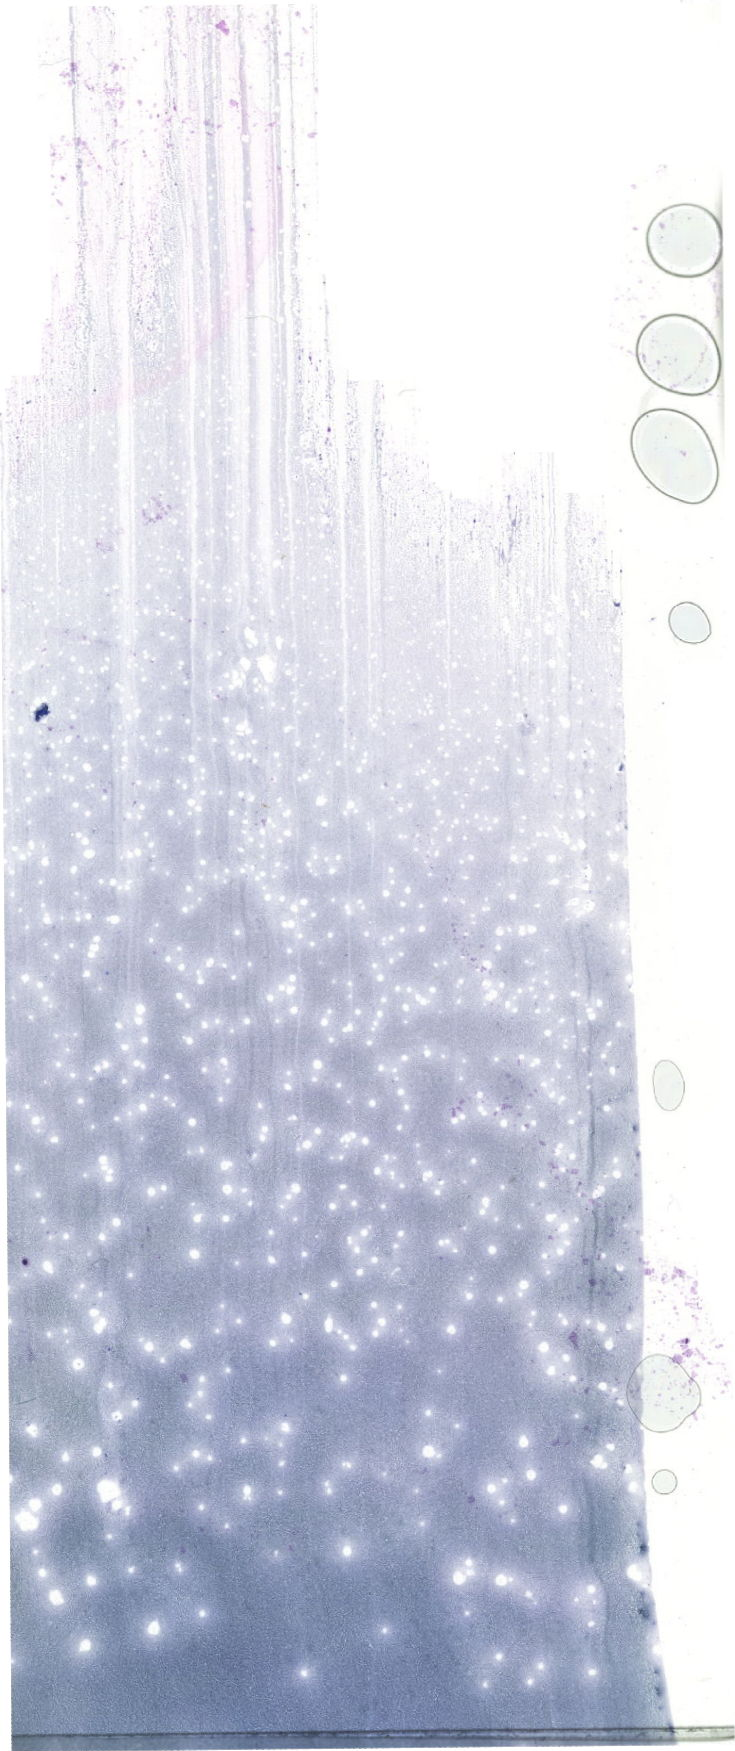
Bone marrow aspirate smear, May-Grünwald-Giemsa (MGG) stain, whole-slide image, whole scanned area (about 20.8 x 49.6 mm) shown as a low-resolution overview. Patient sex: male.
* diagnosis: Acute Megakaryoblastic Leukemia